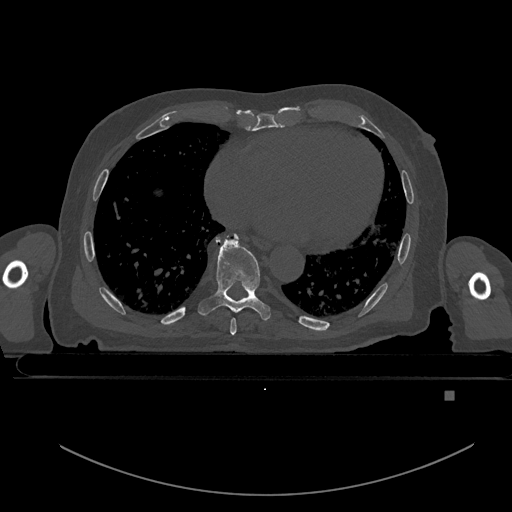
CT including the spine, one axial slice. Slice 205 of 969 in the series (ordered by position). Bone window (W 1800 / L 400 HU). 0.5 mm slice thickness. 512 × 512 image matrix. Patient: male, 82 years. Case-level facts recorded for this patient, not image findings: primary cancer: prostate.
Annotated regions visible in this slice (semi-automatic segmentation, software-assisted and operator-edited):
- T7 vertebra: bounding box <230,318,236,335> (left, top, right, bottom; pixels)
- T8 vertebra: <198,234,272,321>